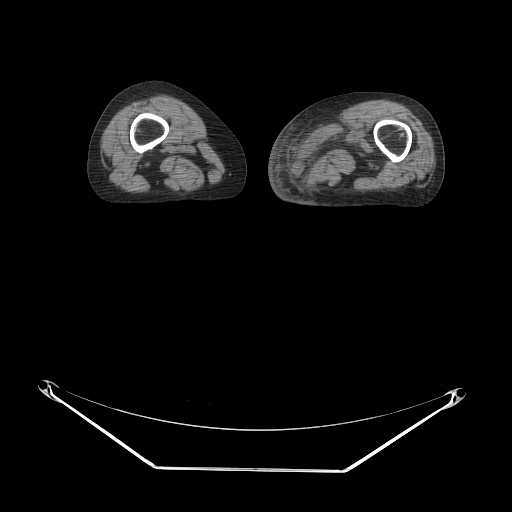
CT of an extremity soft-tissue mass (from a PET/CT study), one axial slice. Slice 10 of 91 in the series (ordered by position). Reconstruction kernel STANDARD. 140 kVp. Soft-tissue window (W 400 / L 40 HU). 3.75 mm slice thickness. 512 × 512 image matrix. Female patient. From the clinical record (not read from this slice): histological type: pleomorphic leiomyosarcoma; grade: high; site of the primary tumour: left thigh.
Structures marked on this image (expert contour drawn on MRI and transferred to this co-registered scan by the dataset authors):
- gross tumour volume including surrounding oedema: bounding box [x1, y1, x2, y2] px = [299, 112, 382, 184]